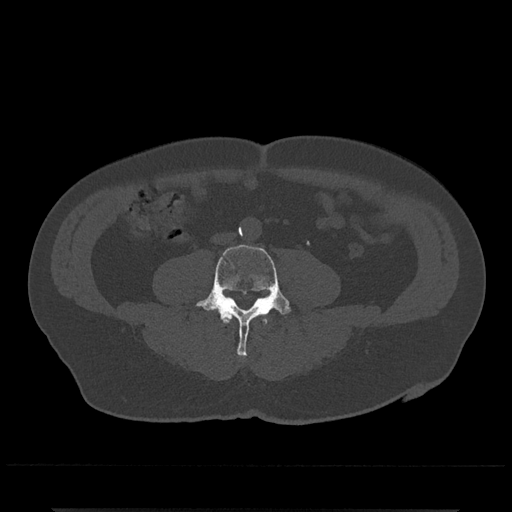
CT including the spine, one axial slice; position 152 of 797 along the scan axis; 120 kVp; bone window (W 1800 / L 400 HU); 0.5 mm slice thickness; 512 × 512 image matrix, field of view 393 × 393 mm. Male patient, age 67 years. From the clinical record (not read from this slice): primary cancer: prostate.
Outlined on this slice (semi-automatically segmented with operator editing):
- L3 vertebra: box from (x=222, y=316) to (x=267, y=324) px
- L4 vertebra: (x=196, y=244)–(x=291, y=357)